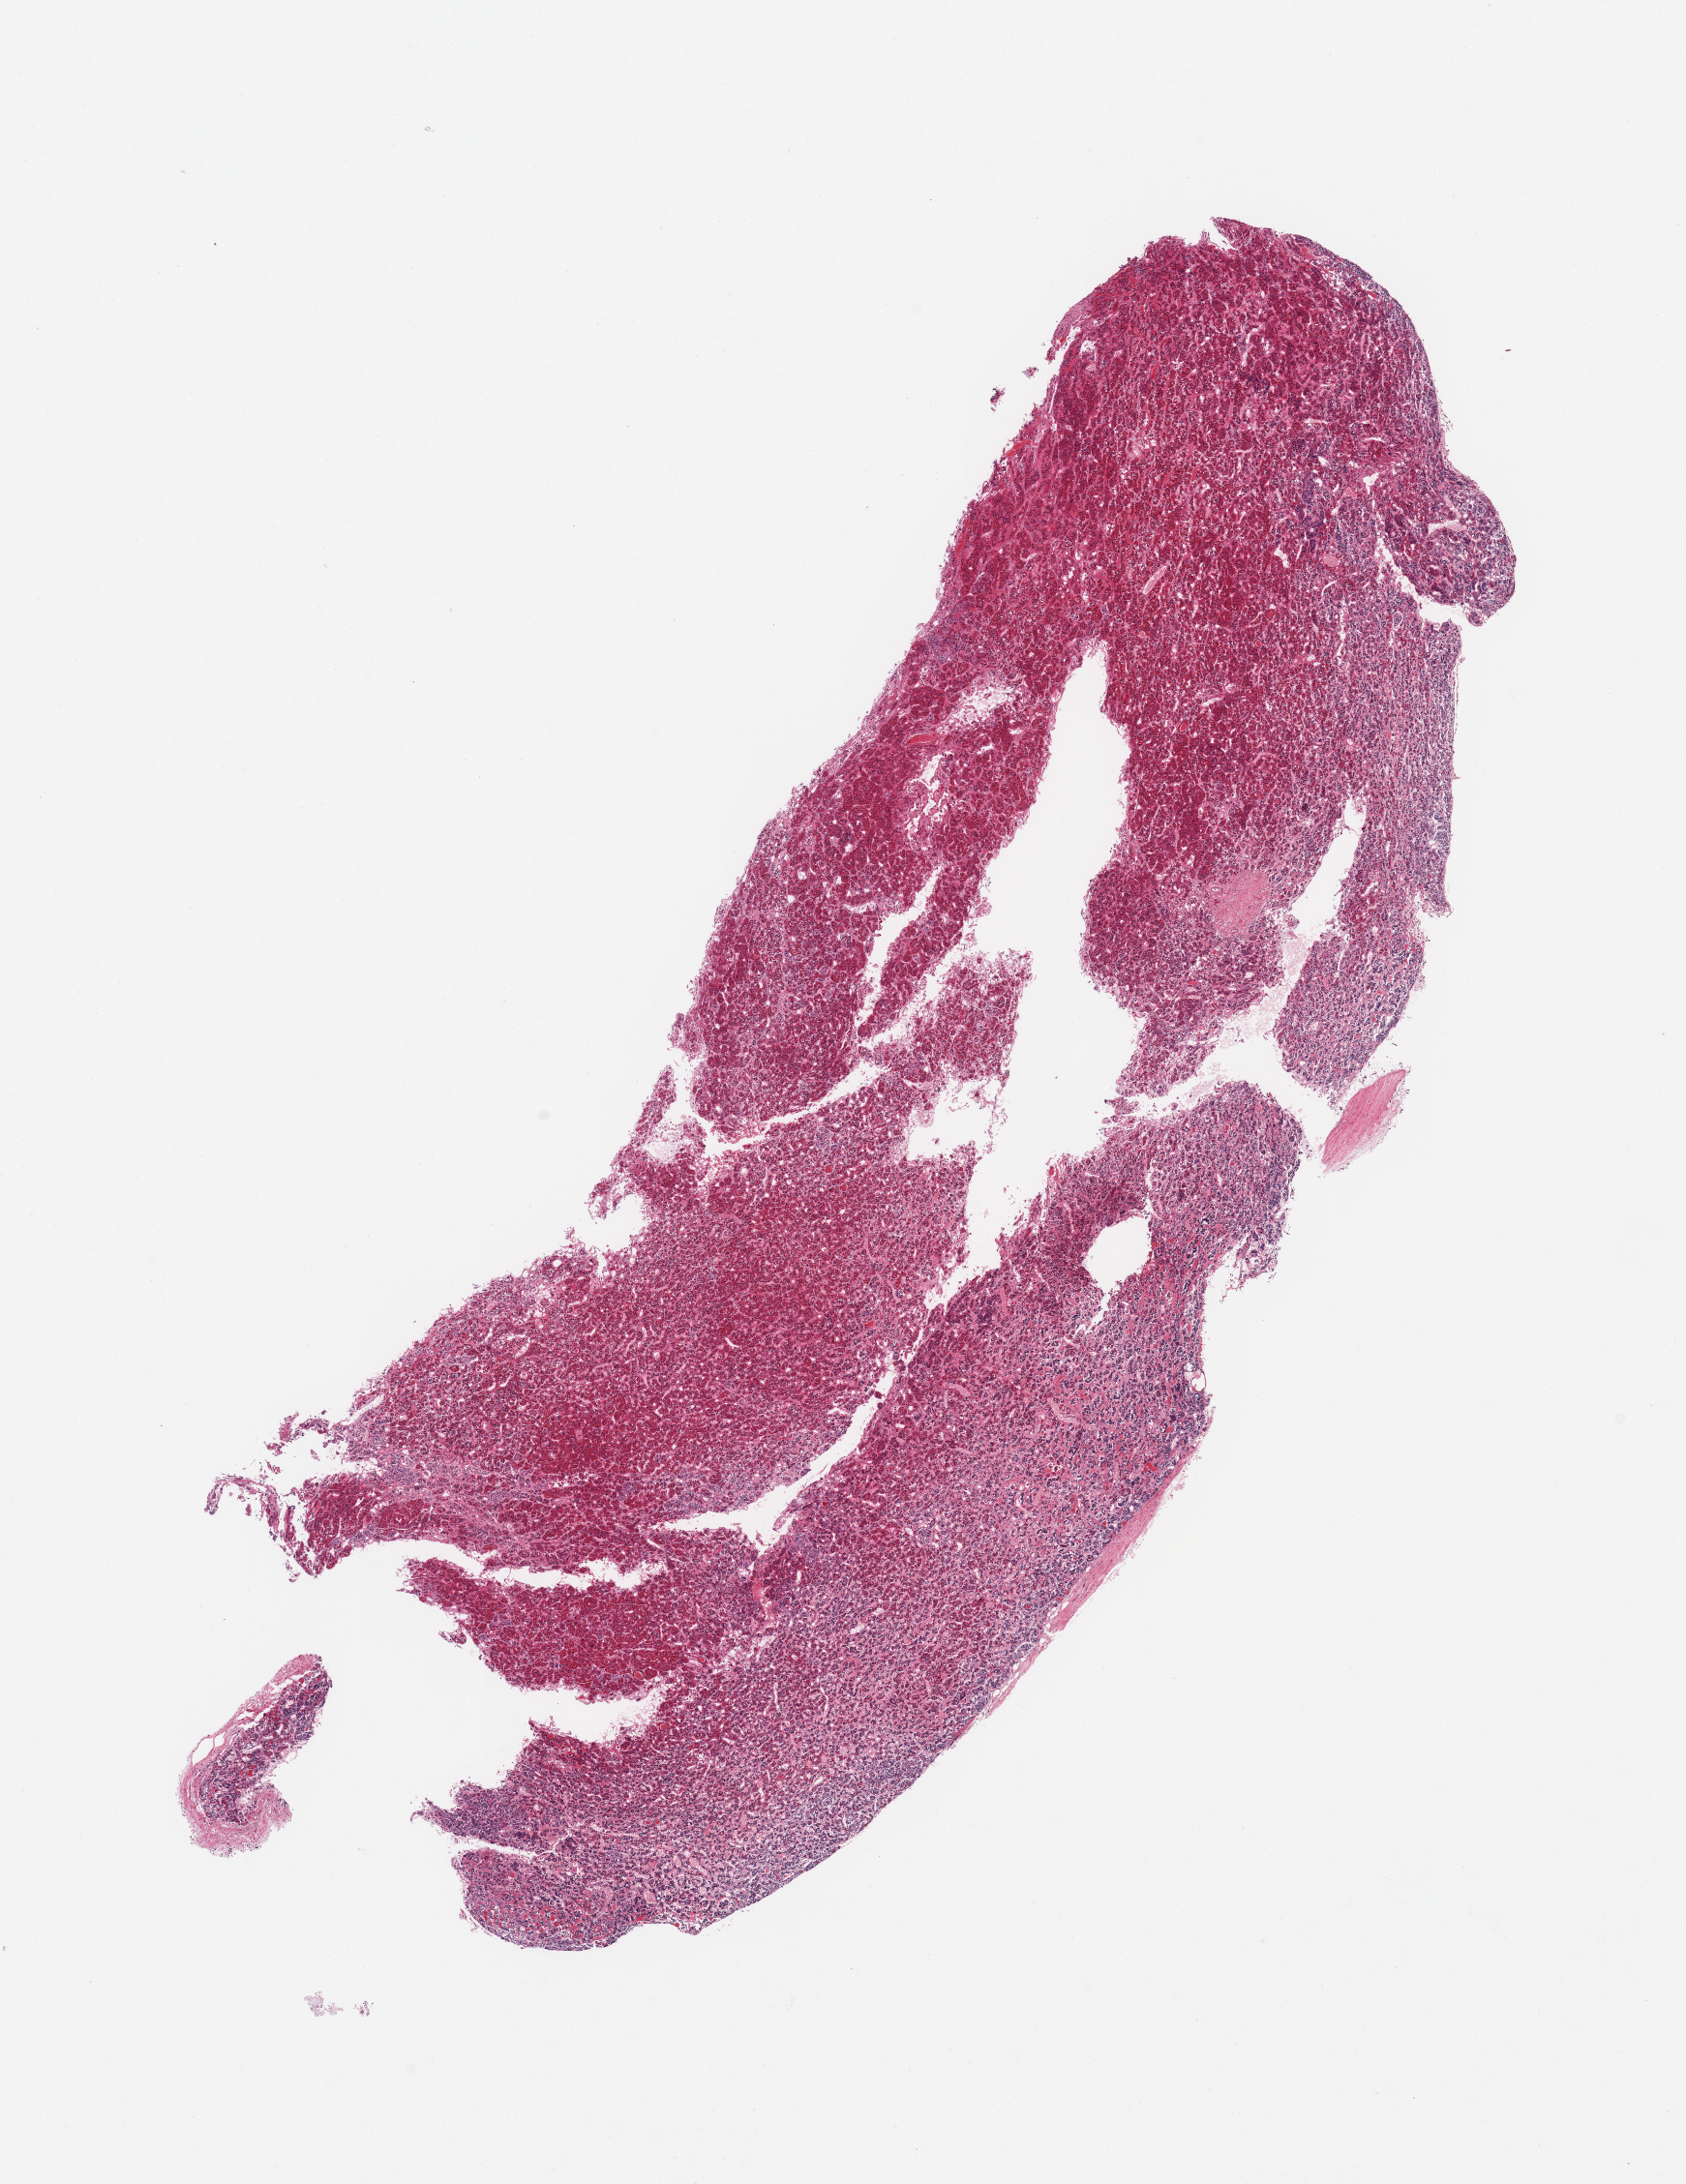
Hematoxylin and eosin (H&E) whole-slide image, brightfield, whole scanned area (about 13.8 x 17.9 mm, acquisition: 20x scan) shown as a low-resolution overview. PAXgene-fixed, paraffin-embedded tissue. Sampled site (target tissue): pituitary. Tissue donor sample. Female donor.
Review note (as recorded): 1 piece, adenohypophysis.